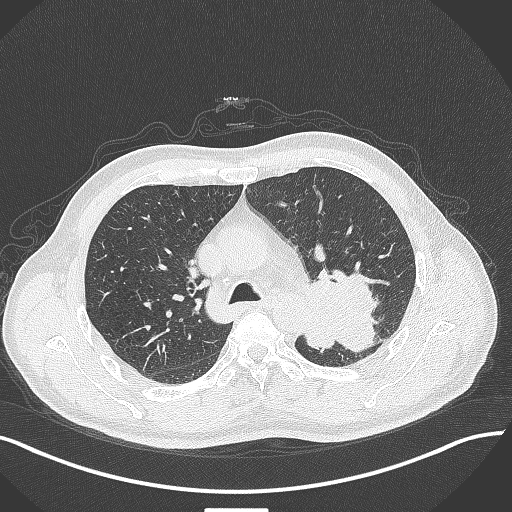
Chest CT, one axial slice; position 287 of 429 along the scan axis; reconstruction kernel B70f; 120 kVp; lung window (W 1500 / L -600 HU); 1 mm slice thickness; 512 × 512 image matrix, field of view 400 × 400 mm. Patient: male, 55 years. Case-level facts recorded for this patient, not image findings: clinical TNM (as recorded): T3 N0 M1c.
Structures marked on this image (bounding box drawn by a radiologist):
- lung tumour (recorded histology: adenocarcinoma): box from (x=304, y=267) to (x=394, y=366) px